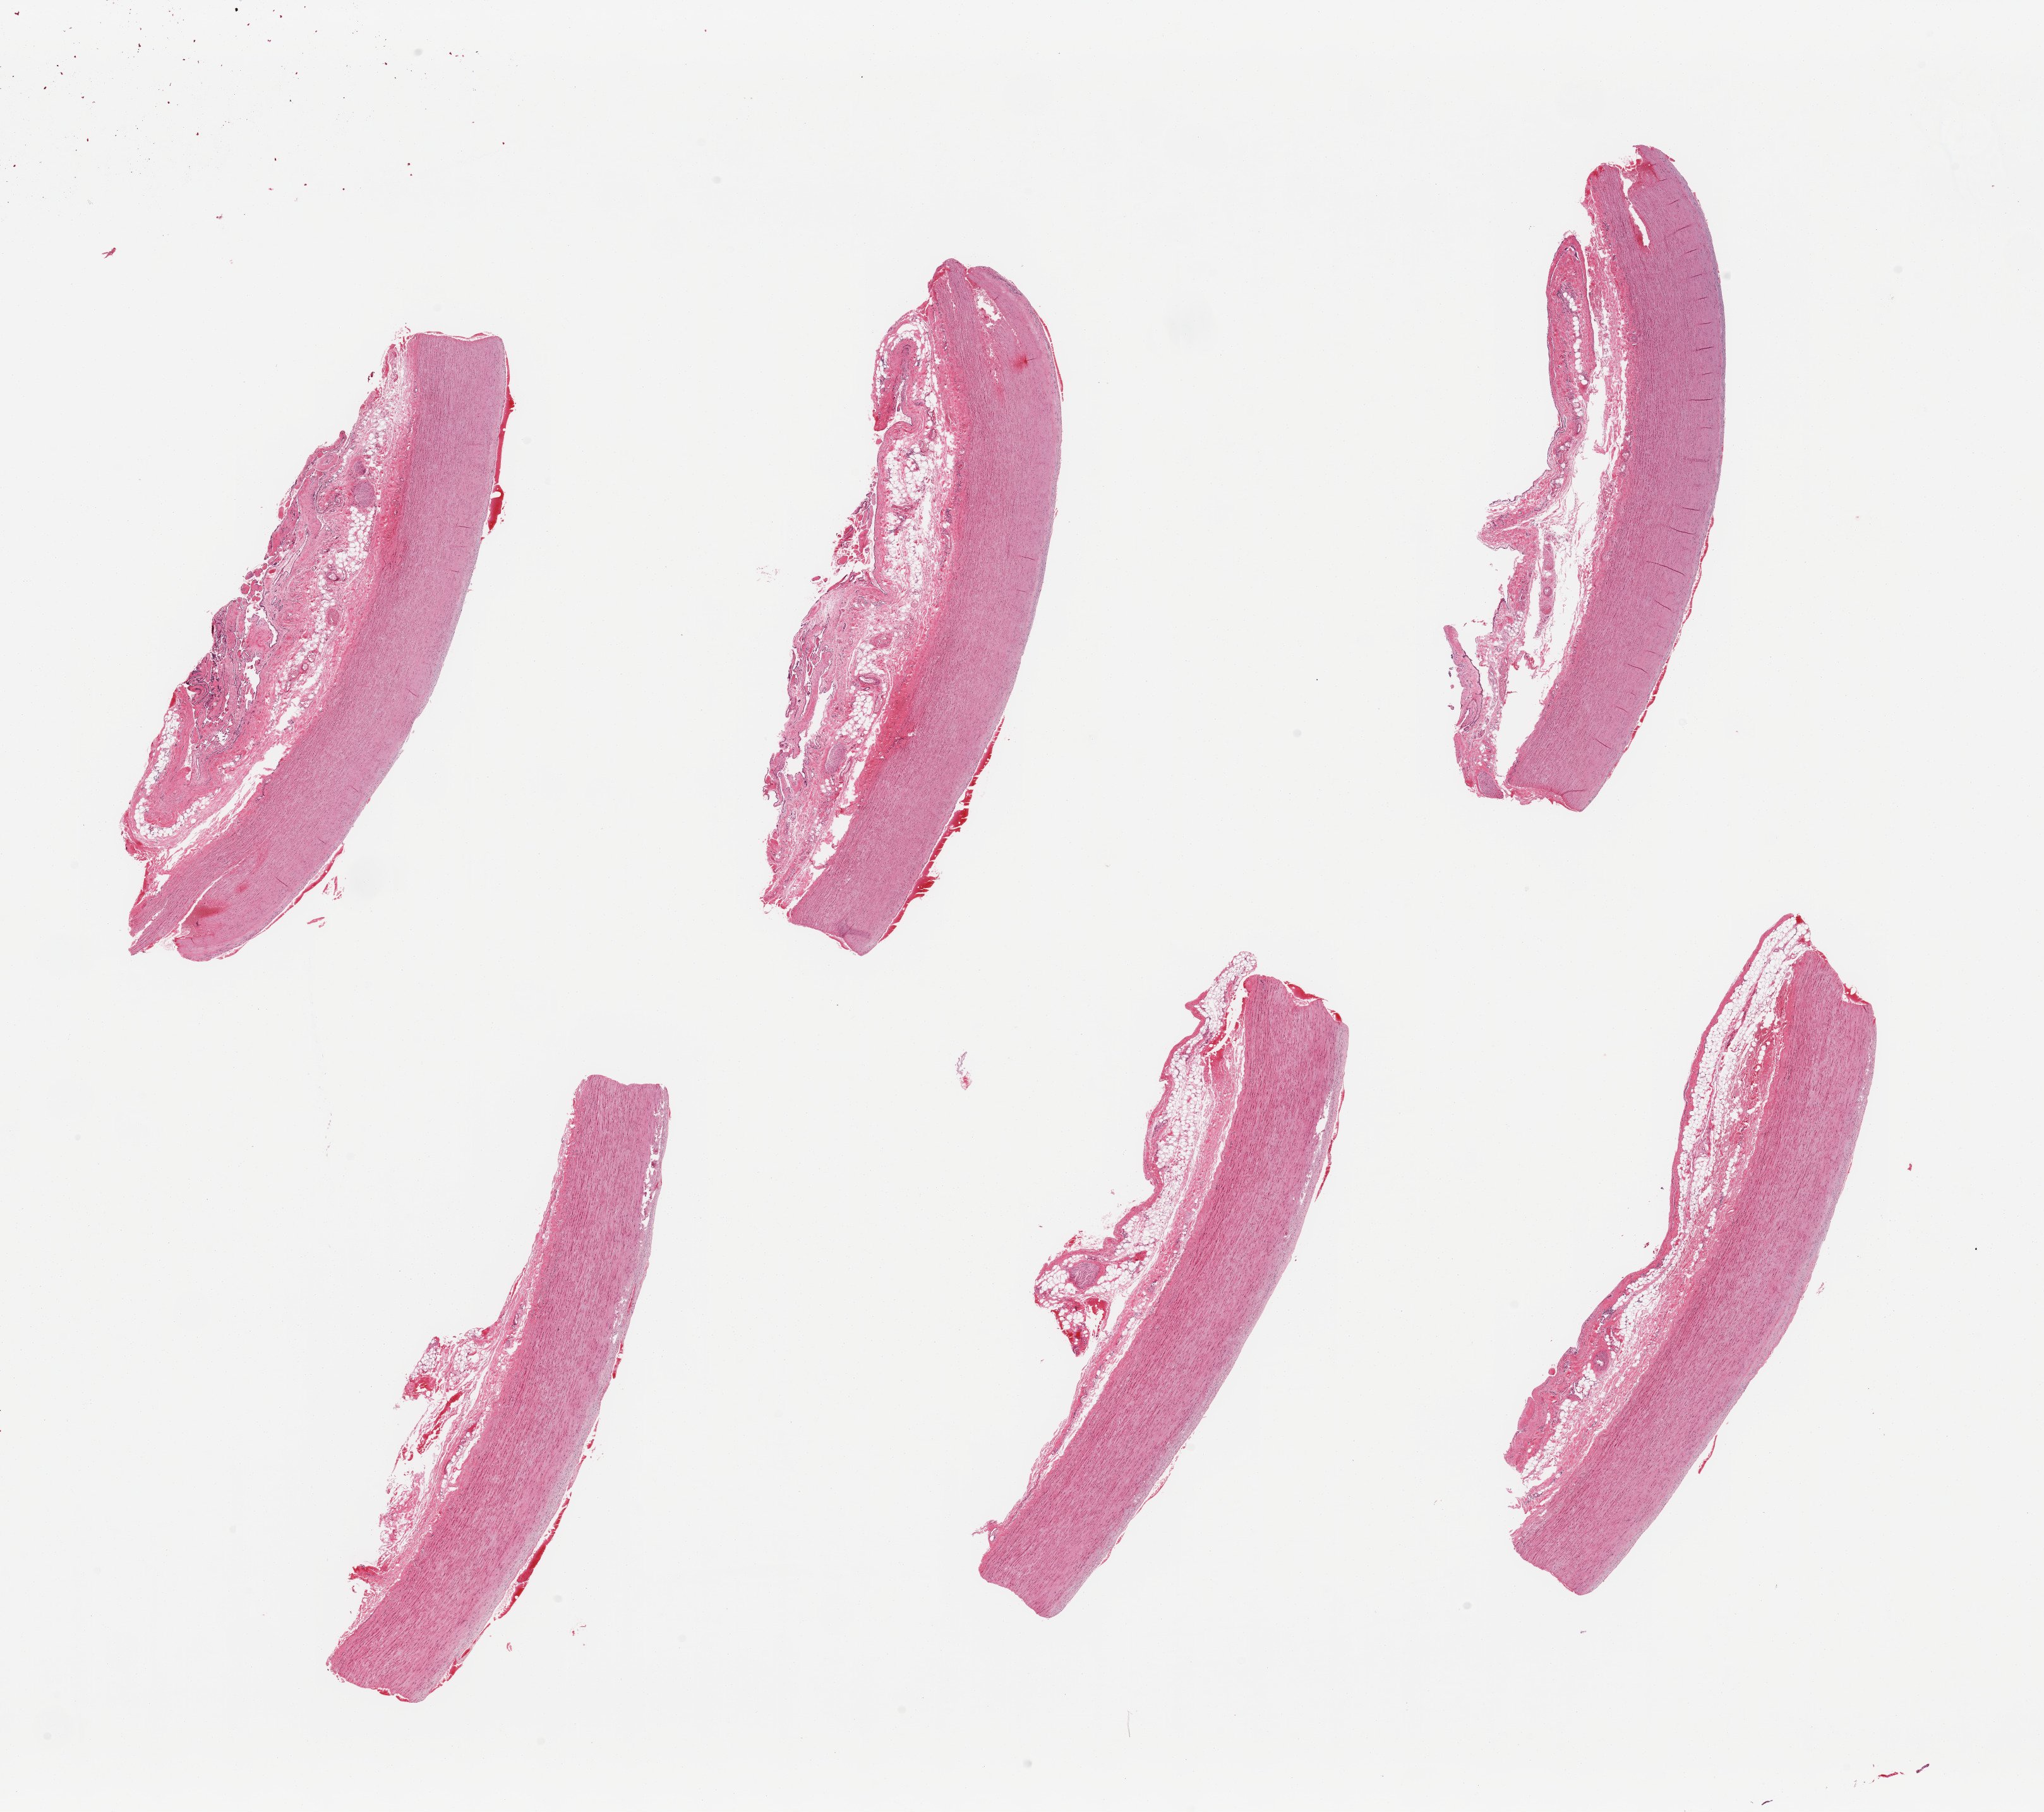
Digitized H&E-stained section, brightfield — a low-resolution overview of the entire scanned area, about 25.6 x 22.7 mm (from a 20x scan); PAXgene-fixed paraffin-embedded (PFPE) section; target tissue: aorta; tissue donor sample. Donor sex: male.
Reviewer comment on this tissue sample: 6 pieces; atherosclerotic plaque.